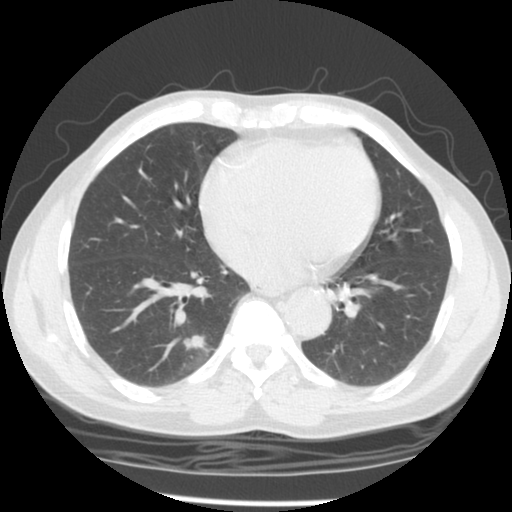
Low-dose screening chest CT, one axial slice; 140 kVp; lung window (W 1500 / L -600 HU); 2.5 mm slice thickness; 512 × 512 image matrix.
Annotated regions visible in this slice (manually delineated by an expert):
- lesion 1 (tumor, lower lobe of right lung): bounding box [x1, y1, x2, y2] px = [184, 335, 206, 349]